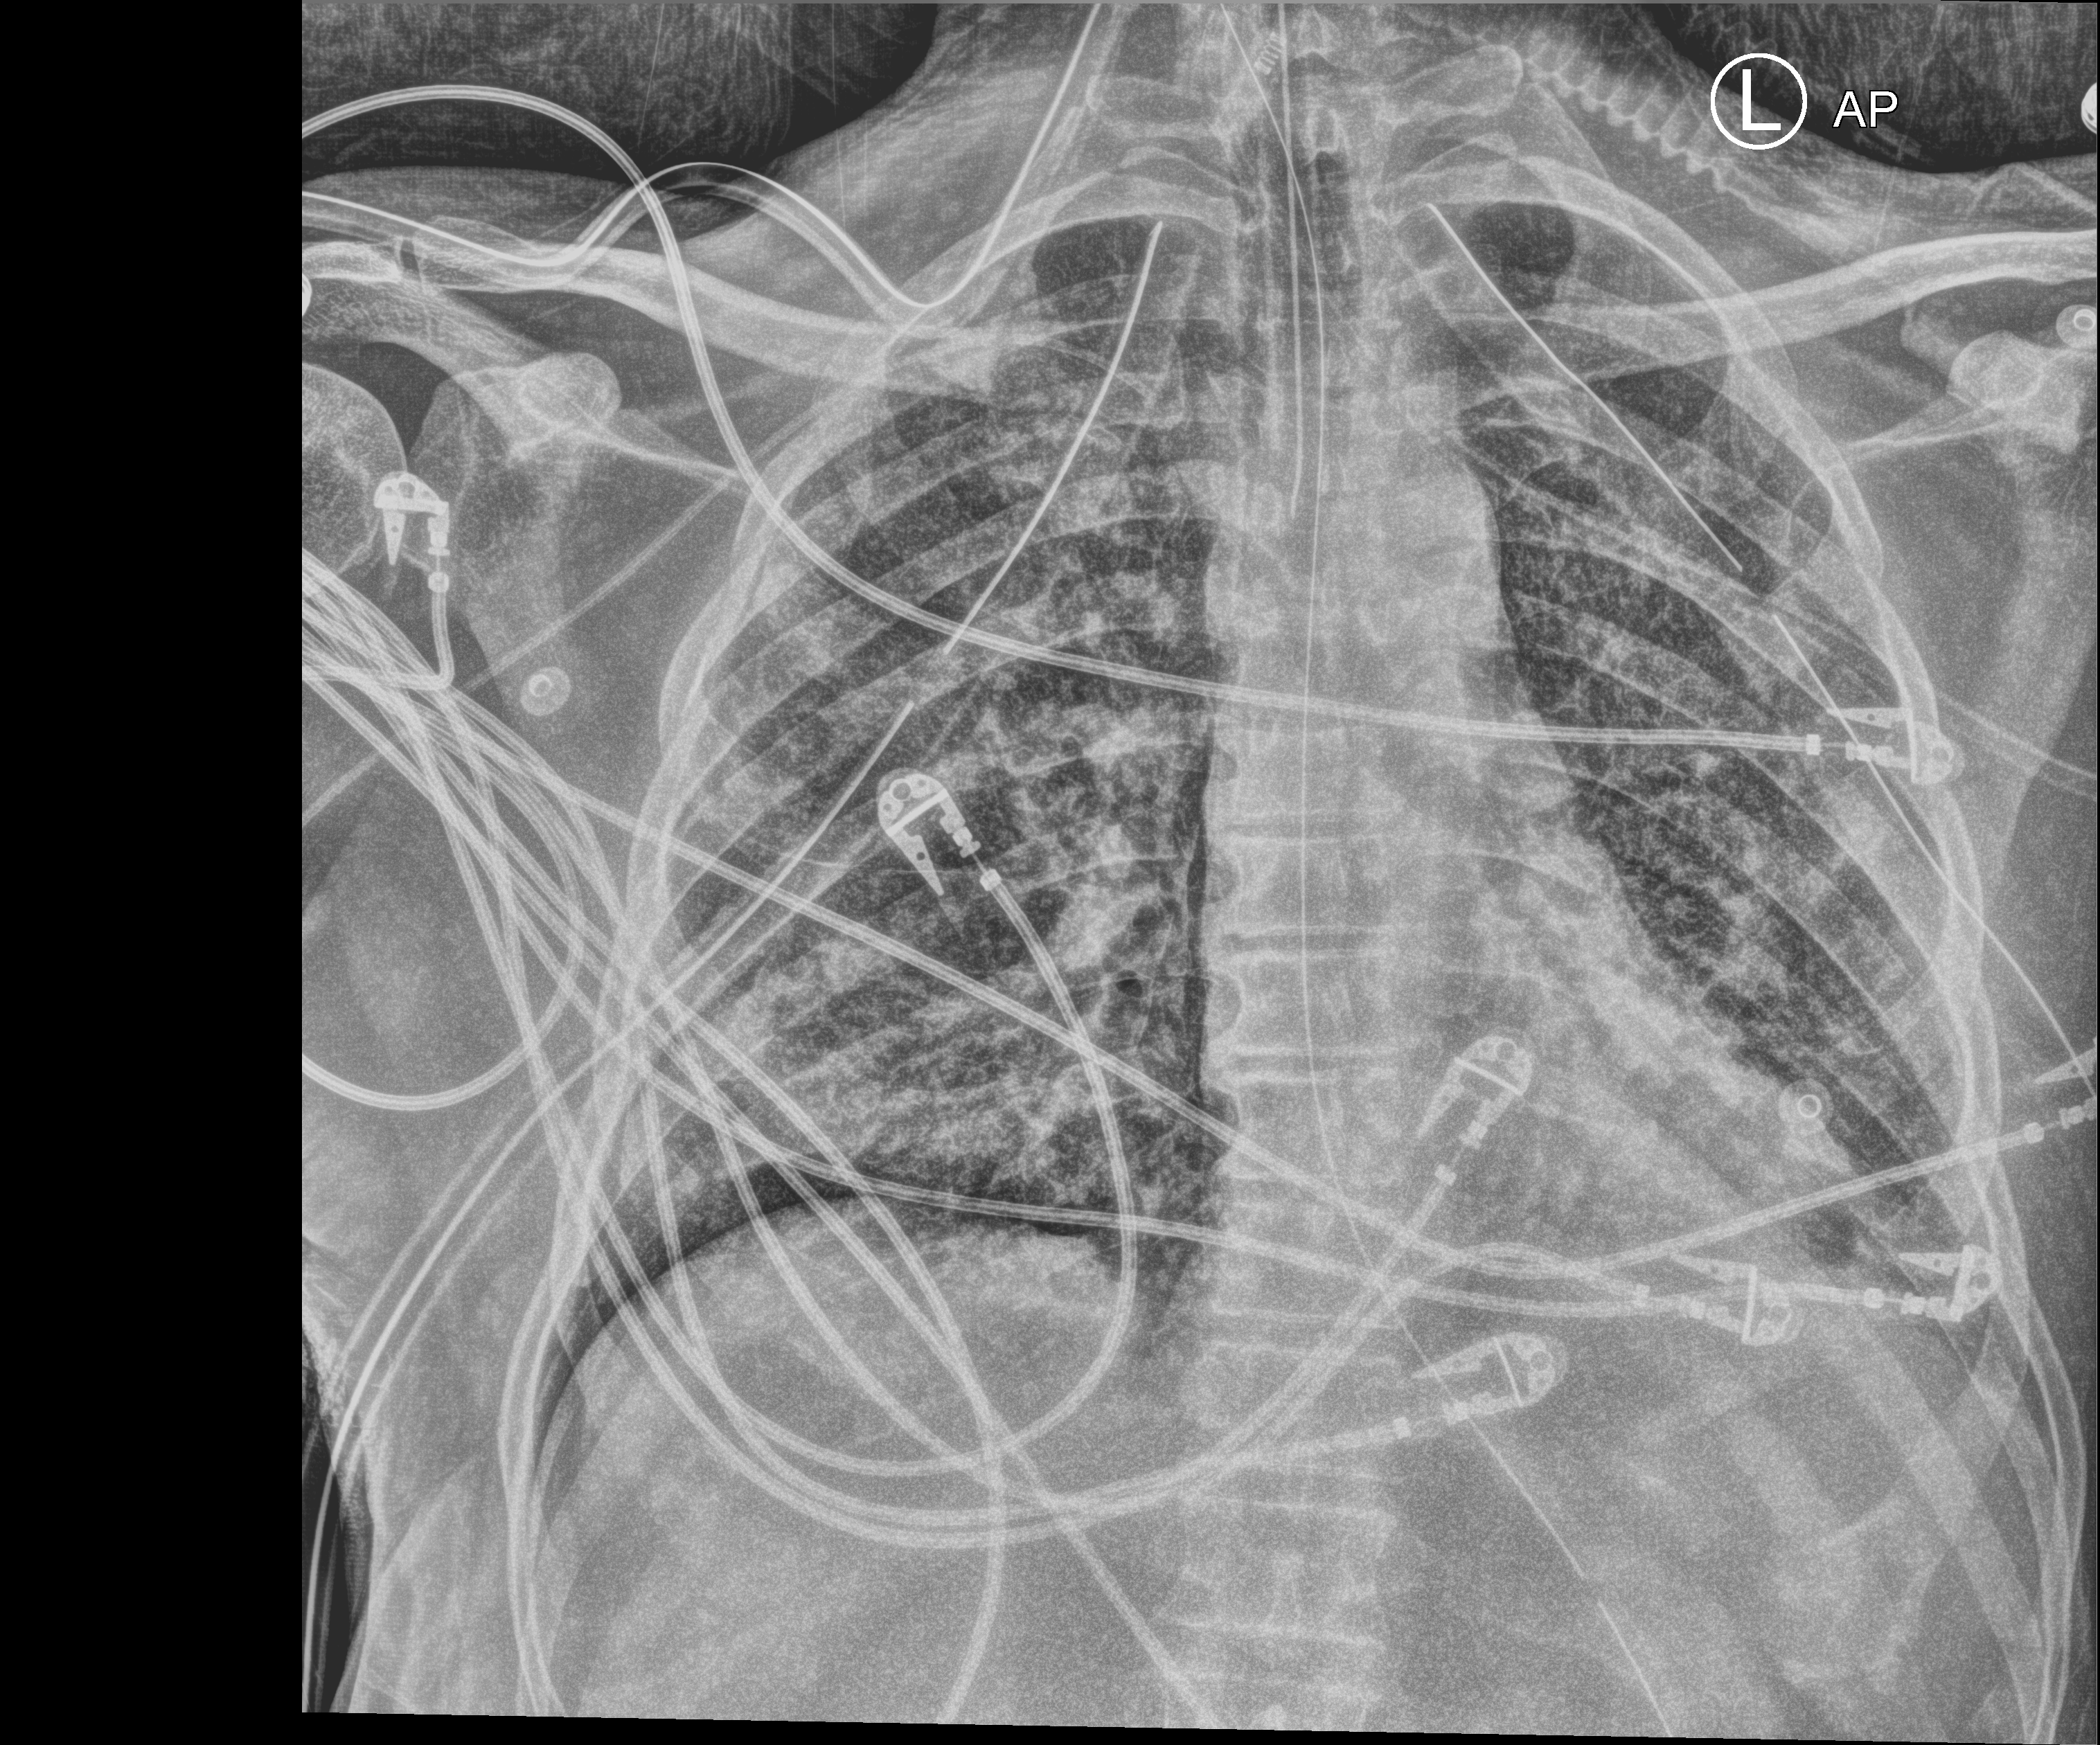
Portable chest radiograph. Patient hospitalised with COVID-19; male, aged 18–59 years.
Hospital-stay facts (about this admission, not read from this image; timing relative to this image not recorded): hypertension (admission record): yes; admitted to intensive care during this hospital stay: yes; chronic kidney disease (admission record): no.